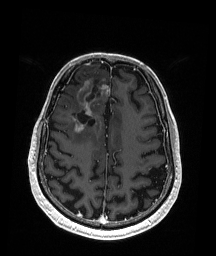
Brain MRI from a brain-tumour surgery series, one axial slice; slice 62 of 192 in the series (ordered by position); T1-weighted post-contrast; 1 mm slice thickness; 216 × 256 image matrix, field of view 211 × 250 mm. From the clinical record (not read from this slice): histopathology: Astrocytoma; WHO grade: 3; IDH mutation: yes.
Structures marked on this image (outlined manually by an expert reader):
- previous resection cavity: bounding box [x1, y1, x2, y2] px = [77, 79, 100, 124]
- tumour: [71, 81, 110, 136]